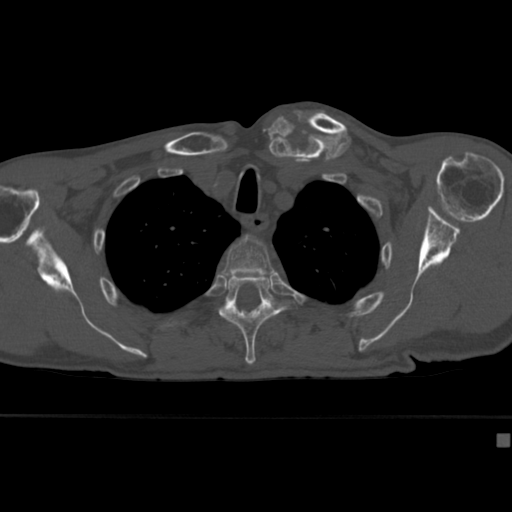
CT including the spine, one axial slice. Slice 323 of 430 in the series (ordered by position). Reconstruction kernel Br40s. 120 kVp. Bone window (W 1800 / L 400 HU). 1.5 mm slice thickness. 512 × 512 image matrix, field of view 337 × 337 mm. Male patient, age 64 years. Case-level facts recorded for this patient, not image findings: primary cancer: uterus; vertebrae with lytic lesions (as recorded): T1, T4, T5, T7, L5.
Structures marked on this image (semi-automatically segmented with operator editing):
- T3 vertebra: bounding box (x1, y1, x2, y2) in pixels: (223, 235, 276, 279)
- T4 vertebra: (219, 274, 291, 365)